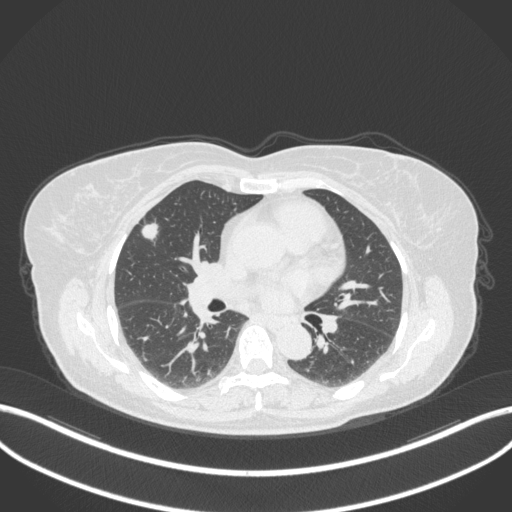
Chest CT, one axial slice. Position 179 of 310 along the scan axis. 120 kVp. Lung window (W 1500 / L -600 HU). 1 mm slice thickness. 512 × 512 image matrix, field of view 400 × 400 mm. Female patient, age 55 years. From the clinical record (not read from this slice): clinical TNM (as recorded): T1b N0 M0; histopathological grade: G2.
Outlined on this slice (rectangle marked by the reading radiologist):
- lung tumour (recorded histology: adenocarcinoma): bounding box <136,218,160,247> (left, top, right, bottom; pixels)